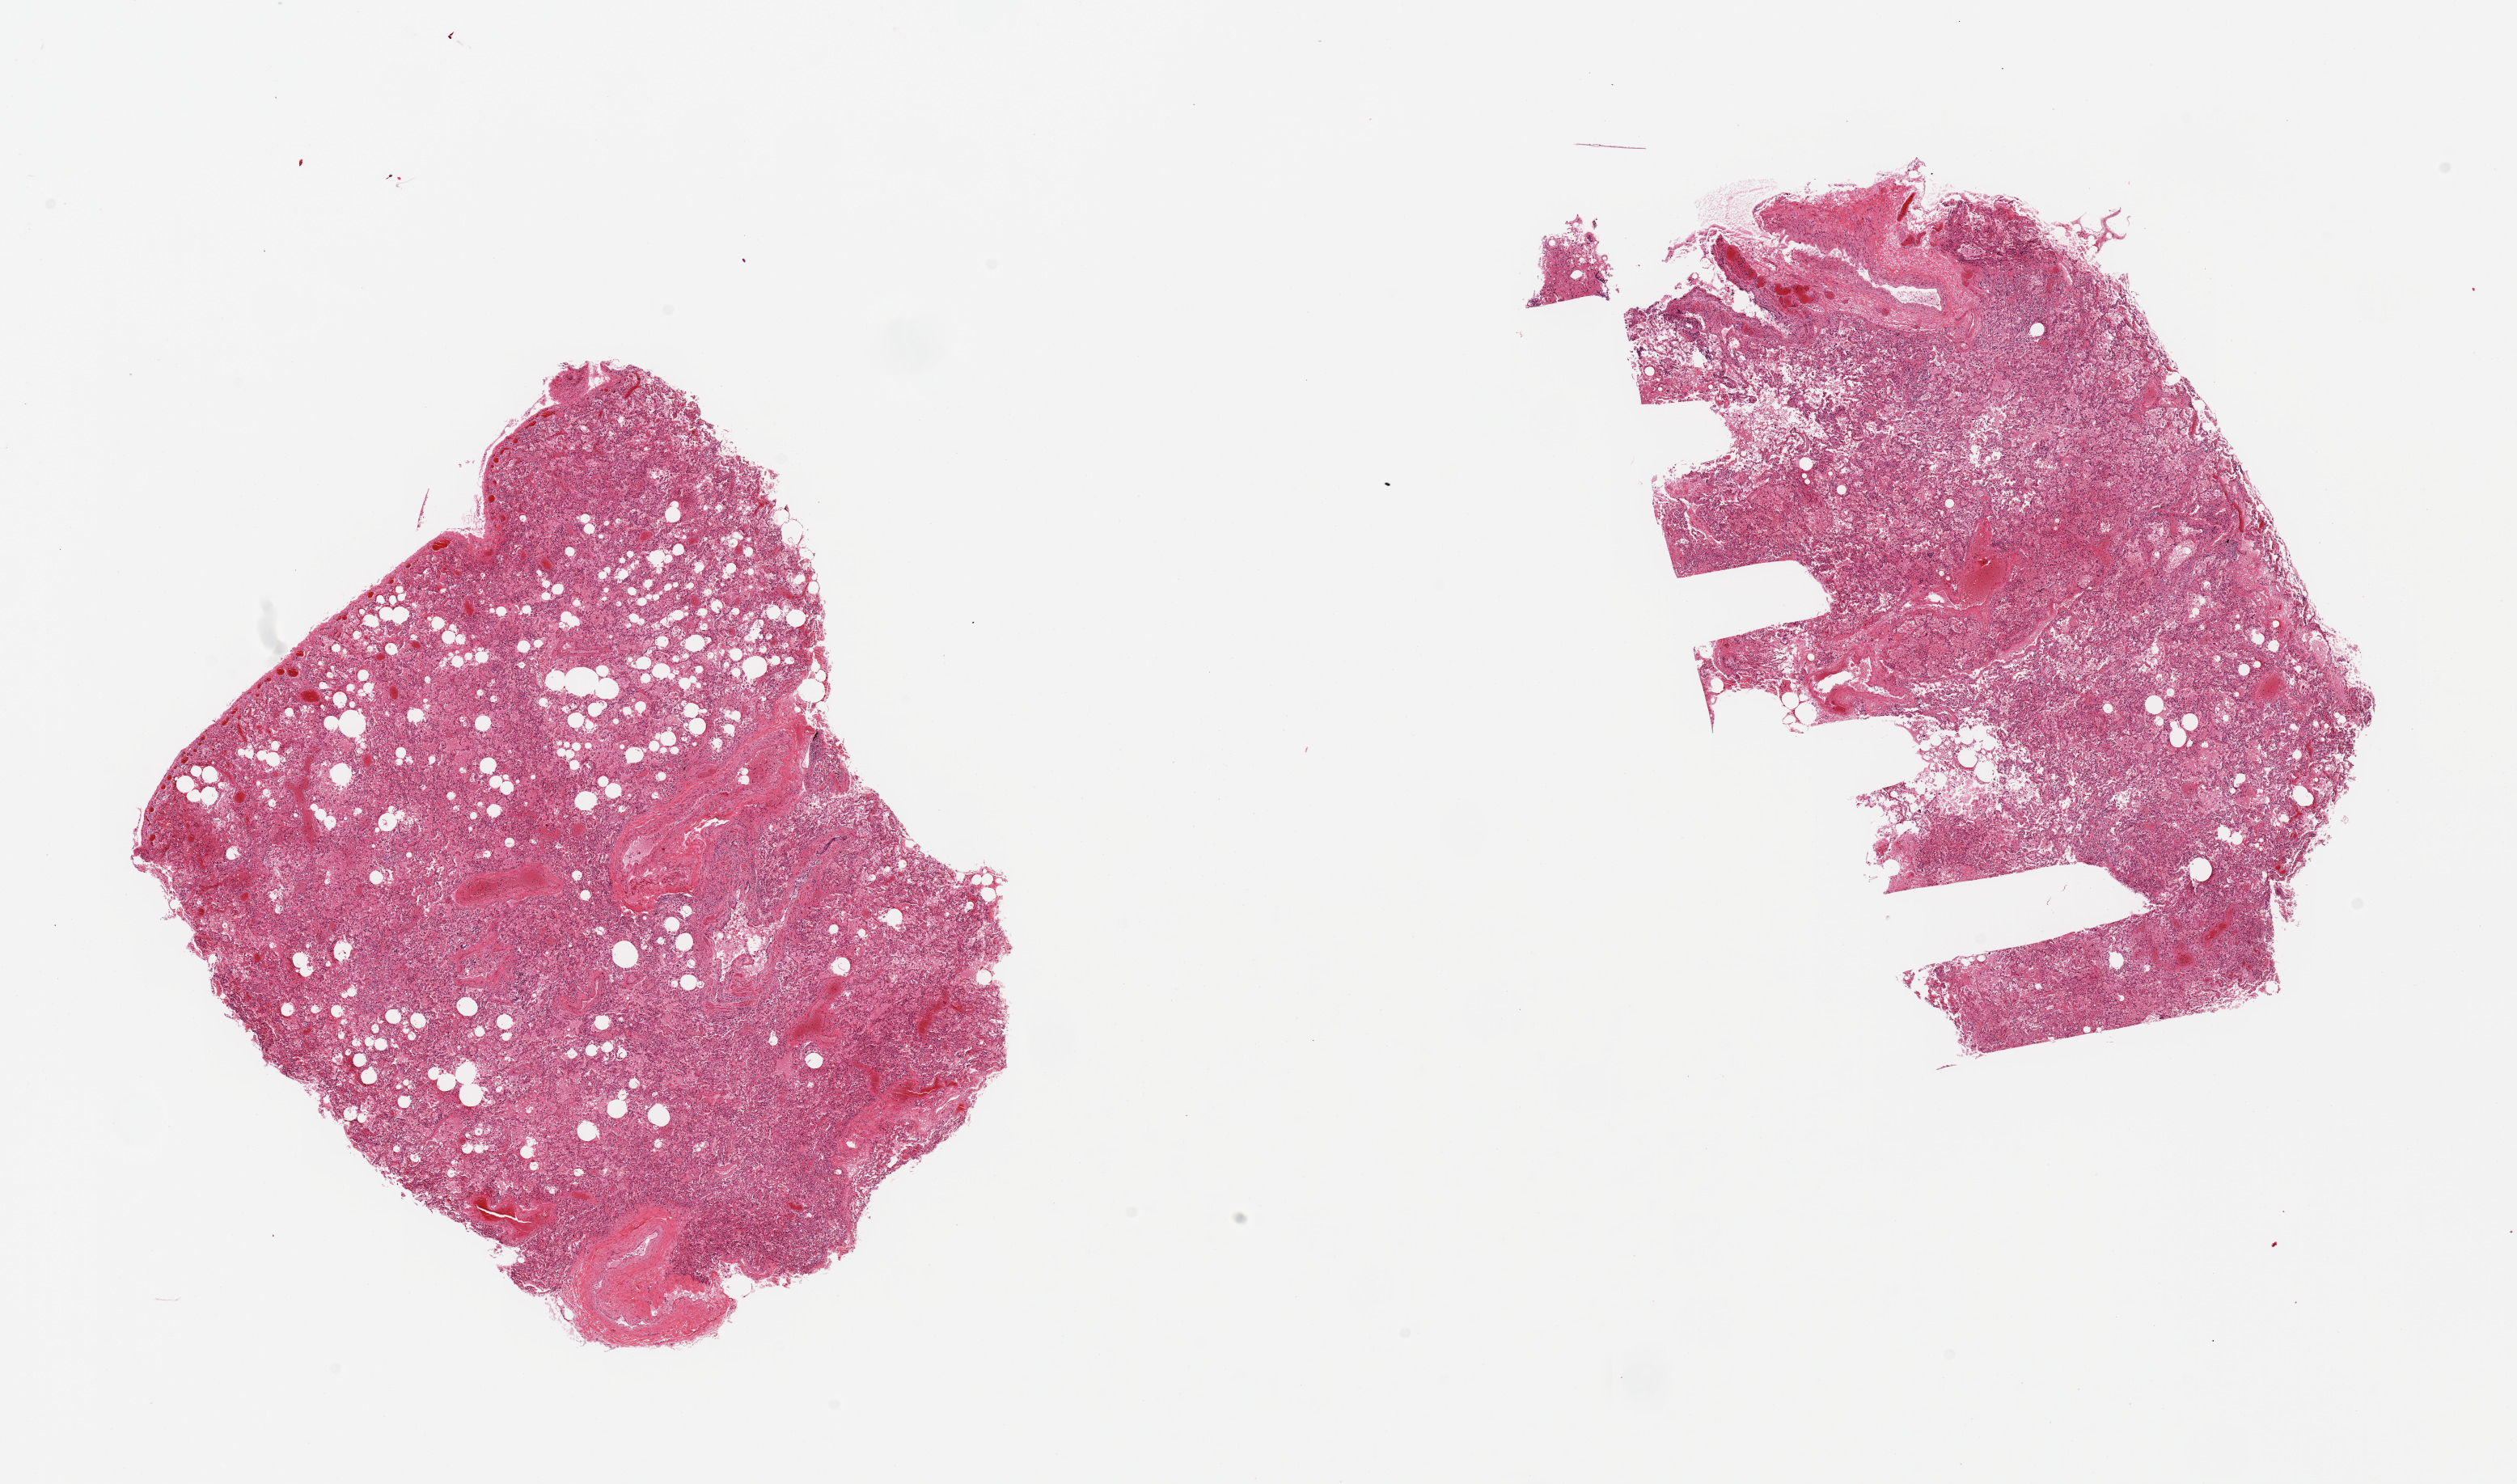
Haematoxylin and eosin whole-slide image, low-resolution overview of the scanned area, about 24.6 x 14.5 mm (slide scanned at 20x); PAXgene-fixed paraffin-embedded (PFPE) section; sampled site (target tissue): lung; donor tissue sample. Male donor.
Pathologist's review note for this sample: 2 pieces; marked congestion and large vessels included.